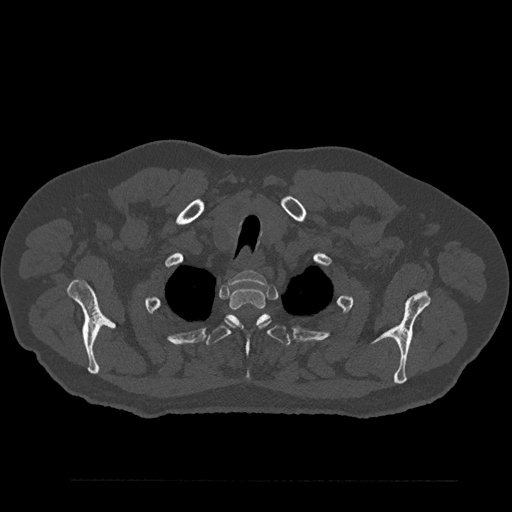
CT including the spine, one axial slice. Position 707 of 797 along the scan axis. Reconstruction kernel Br40s/3. Bone window (W 1800 / L 400 HU). 0.5 mm slice thickness. 512 × 512 image matrix, field of view 430 × 430 mm. Male patient, age 61 years. From the clinical record (not read from this slice): primary cancer: prostate.
Annotated regions visible in this slice (semi-automatic segmentation, software-assisted and operator-edited):
- T1 vertebra: bounding box (x1, y1, x2, y2) in pixels: (228, 271, 267, 285)
- T2 vertebra: (229, 288, 269, 328)
- T3 vertebra: (206, 314, 290, 380)